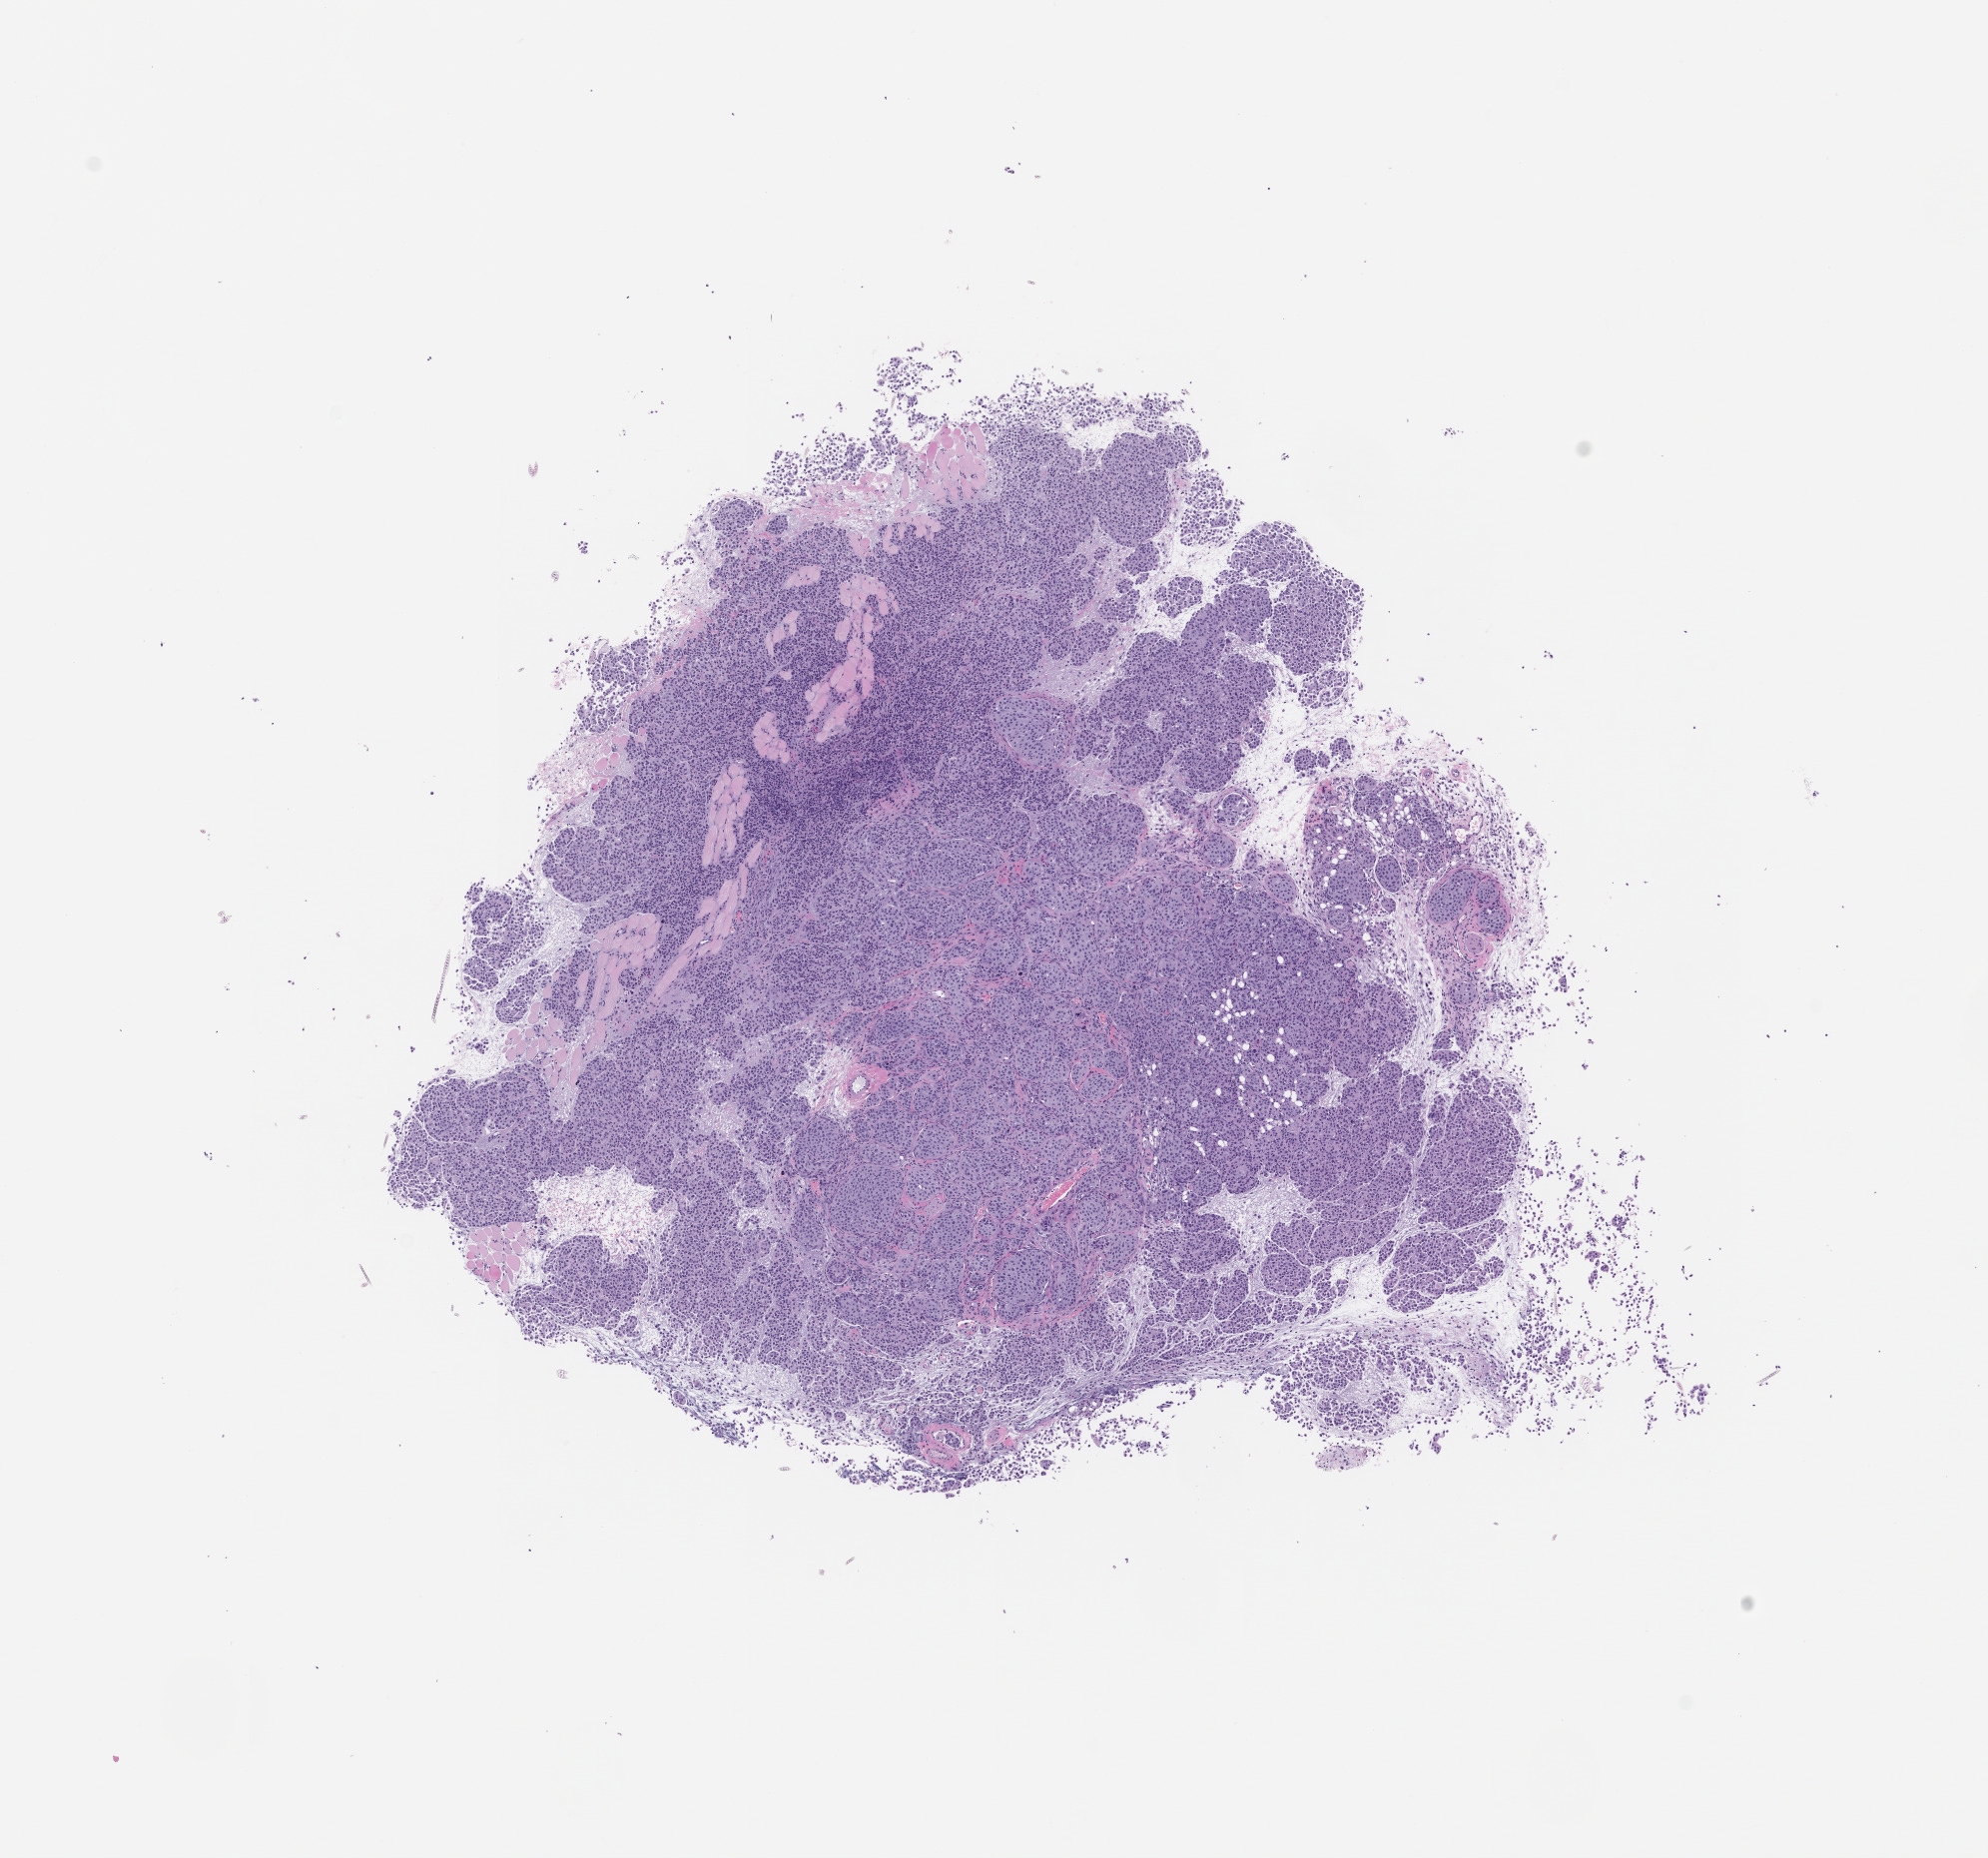
Hematoxylin and eosin (H&E) whole-slide image of a patient-derived xenograft (PDX) tumor grown in a mouse, passage 2 — a low-resolution overview of the entire scanned area, about 8.0 x 7.5 mm, formalin-fixed paraffin-embedded section, originating tumor site category: bladder.
Originating patient diagnosis: Transitional Cell Carcinoma.